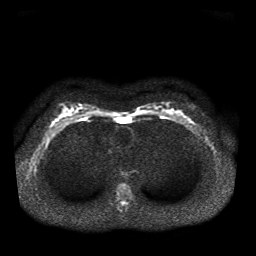
Breast MRI, one axial slice; position 23 of 41 along the scan axis; diffusion-weighted series; image 2 of 4 stored at this slice position (different b-values; order by instance number); 1.5 T; 5 mm slice thickness; 256 × 256 image matrix, field of view 330 × 330 mm. Female patient.
Outlined on this slice (outlined manually by an expert reader):
- tumour on diffusion-weighted imaging: bounding box [x1, y1, x2, y2] px = [185, 117, 191, 121]